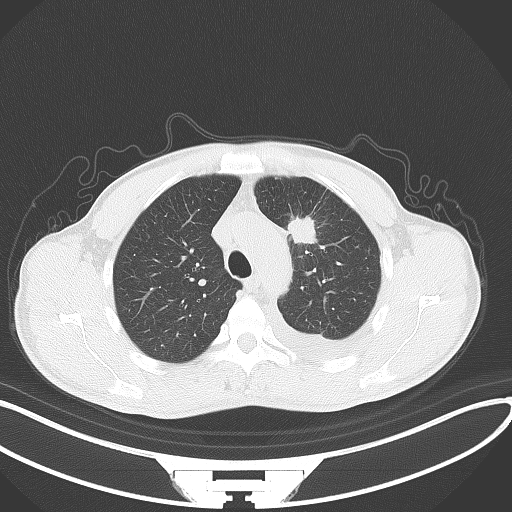
Chest CT, one axial slice. Slice 99 of 130 in the series (ordered by position). 120 kVp. Lung window (W 1500 / L -600 HU). 3 mm slice thickness. 512 × 512 image matrix, field of view 400 × 400 mm. Patient: male, 49 years. Case-level facts recorded for this patient, not image findings: clinical TNM (as recorded): T1c N1 M1.
Structures marked on this image (bounding box drawn by a radiologist):
- lung tumour (recorded histology: adenocarcinoma): bounding box (x1, y1, x2, y2) in pixels: (287, 216, 322, 250)